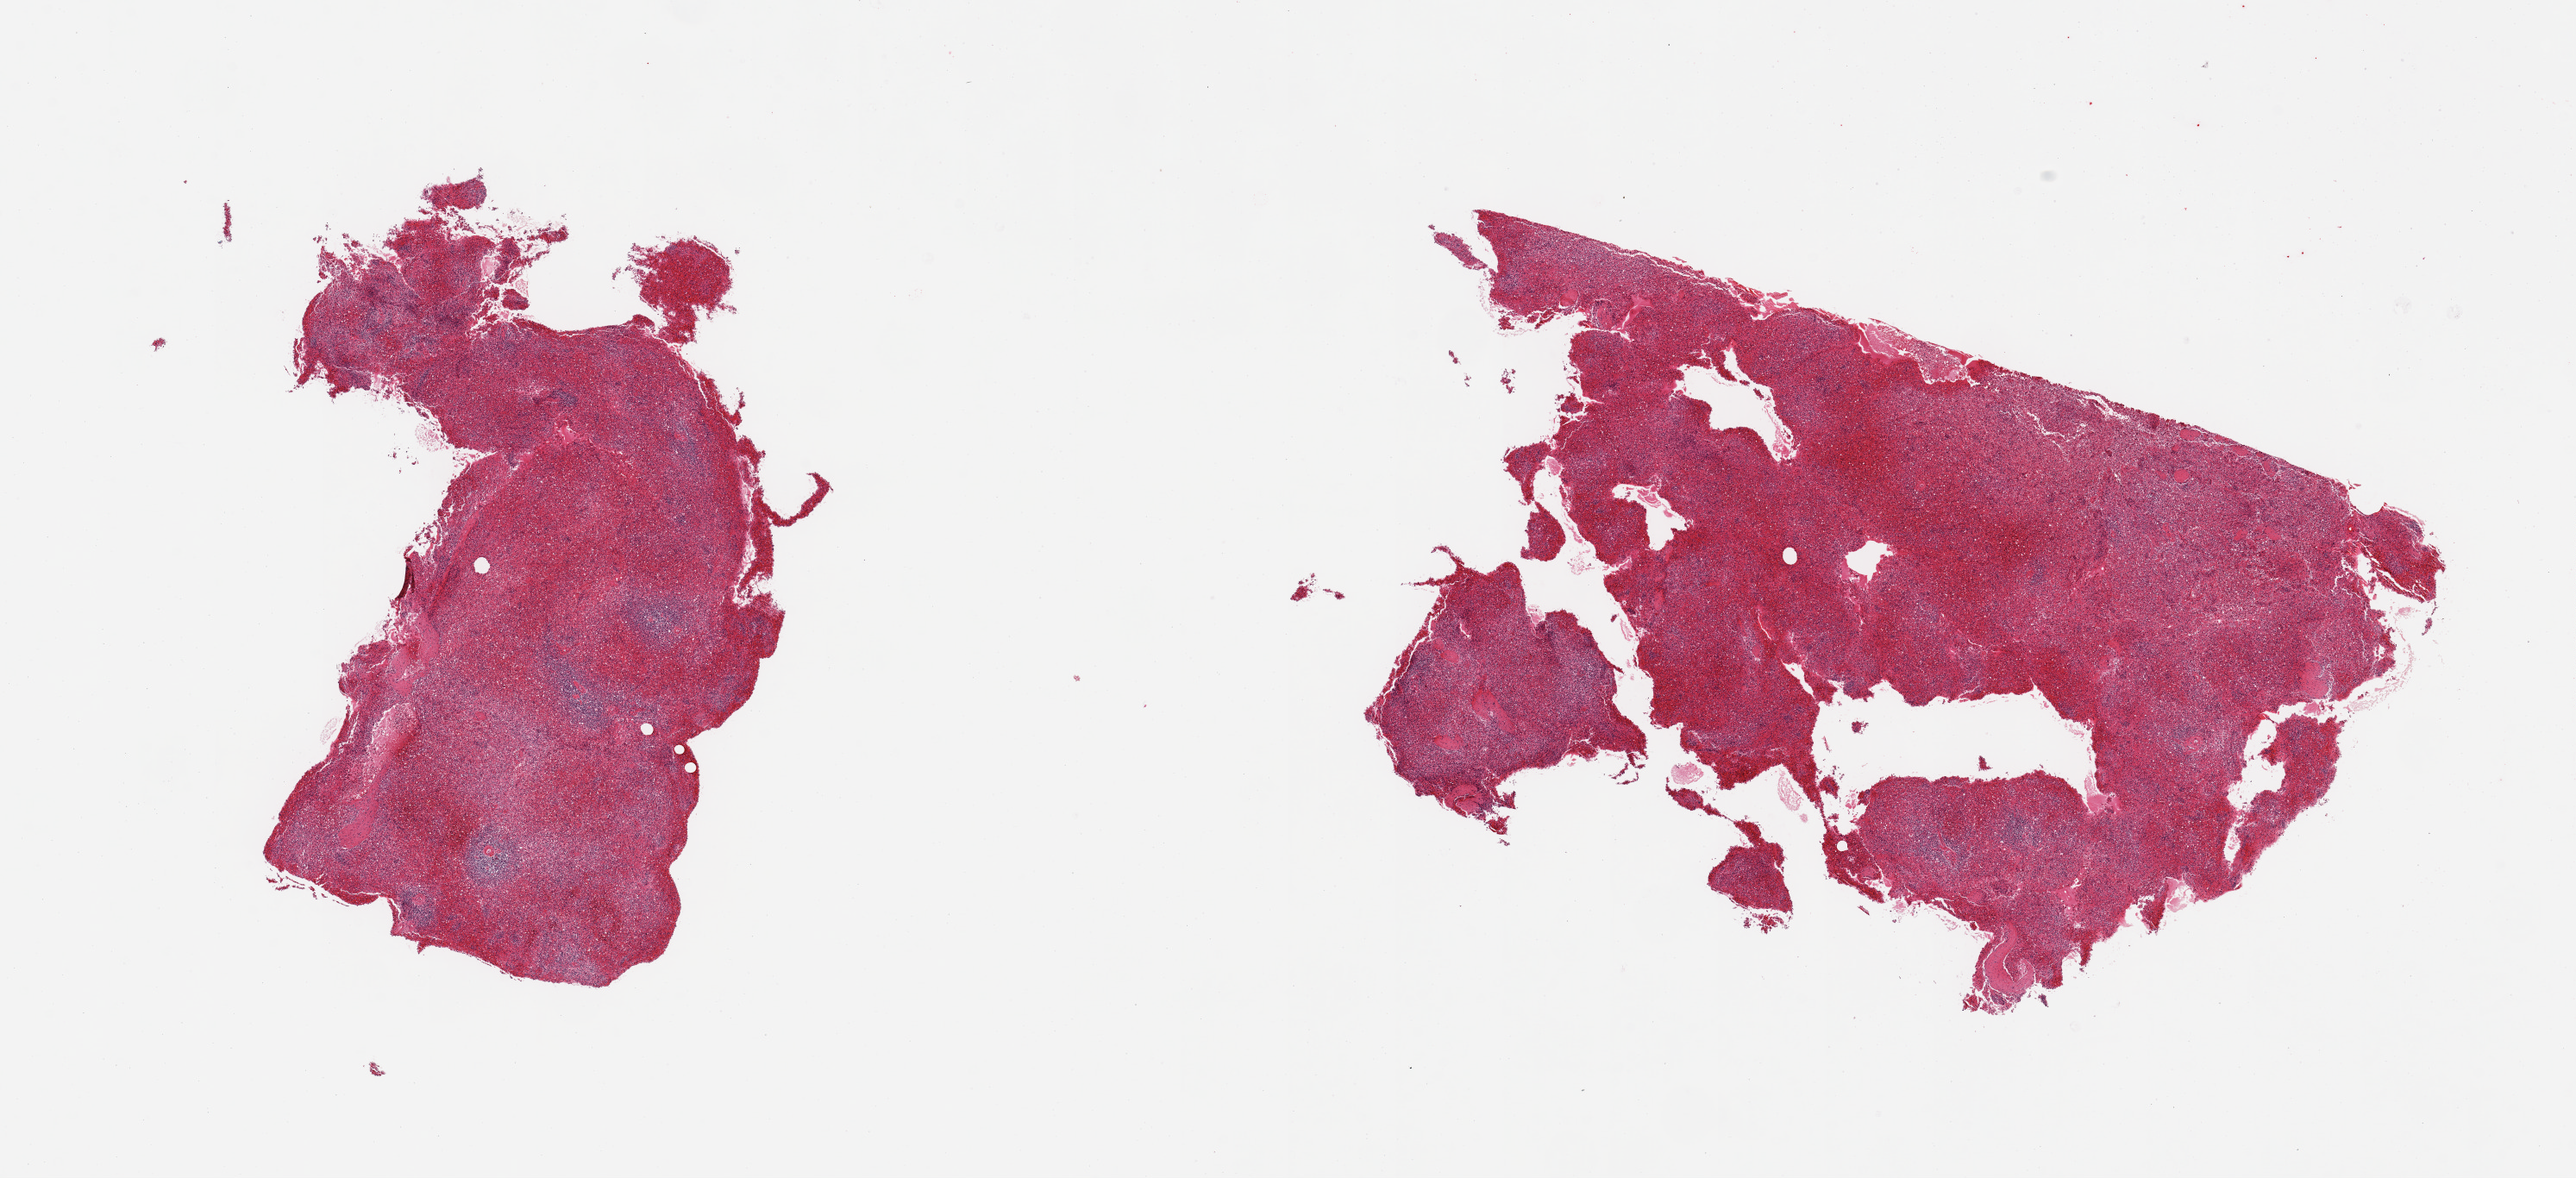
Haematoxylin and eosin whole-slide image, brightfield — whole scanned area (about 23.6 x 10.8 mm) shown as a low-resolution overview, PAXgene-fixed paraffin-embedded (PFPE) section, sampled site (target tissue): spleen, donor tissue sample. Donor: female.
• reviewer comment on this tissue sample: 2 pieces; congestion